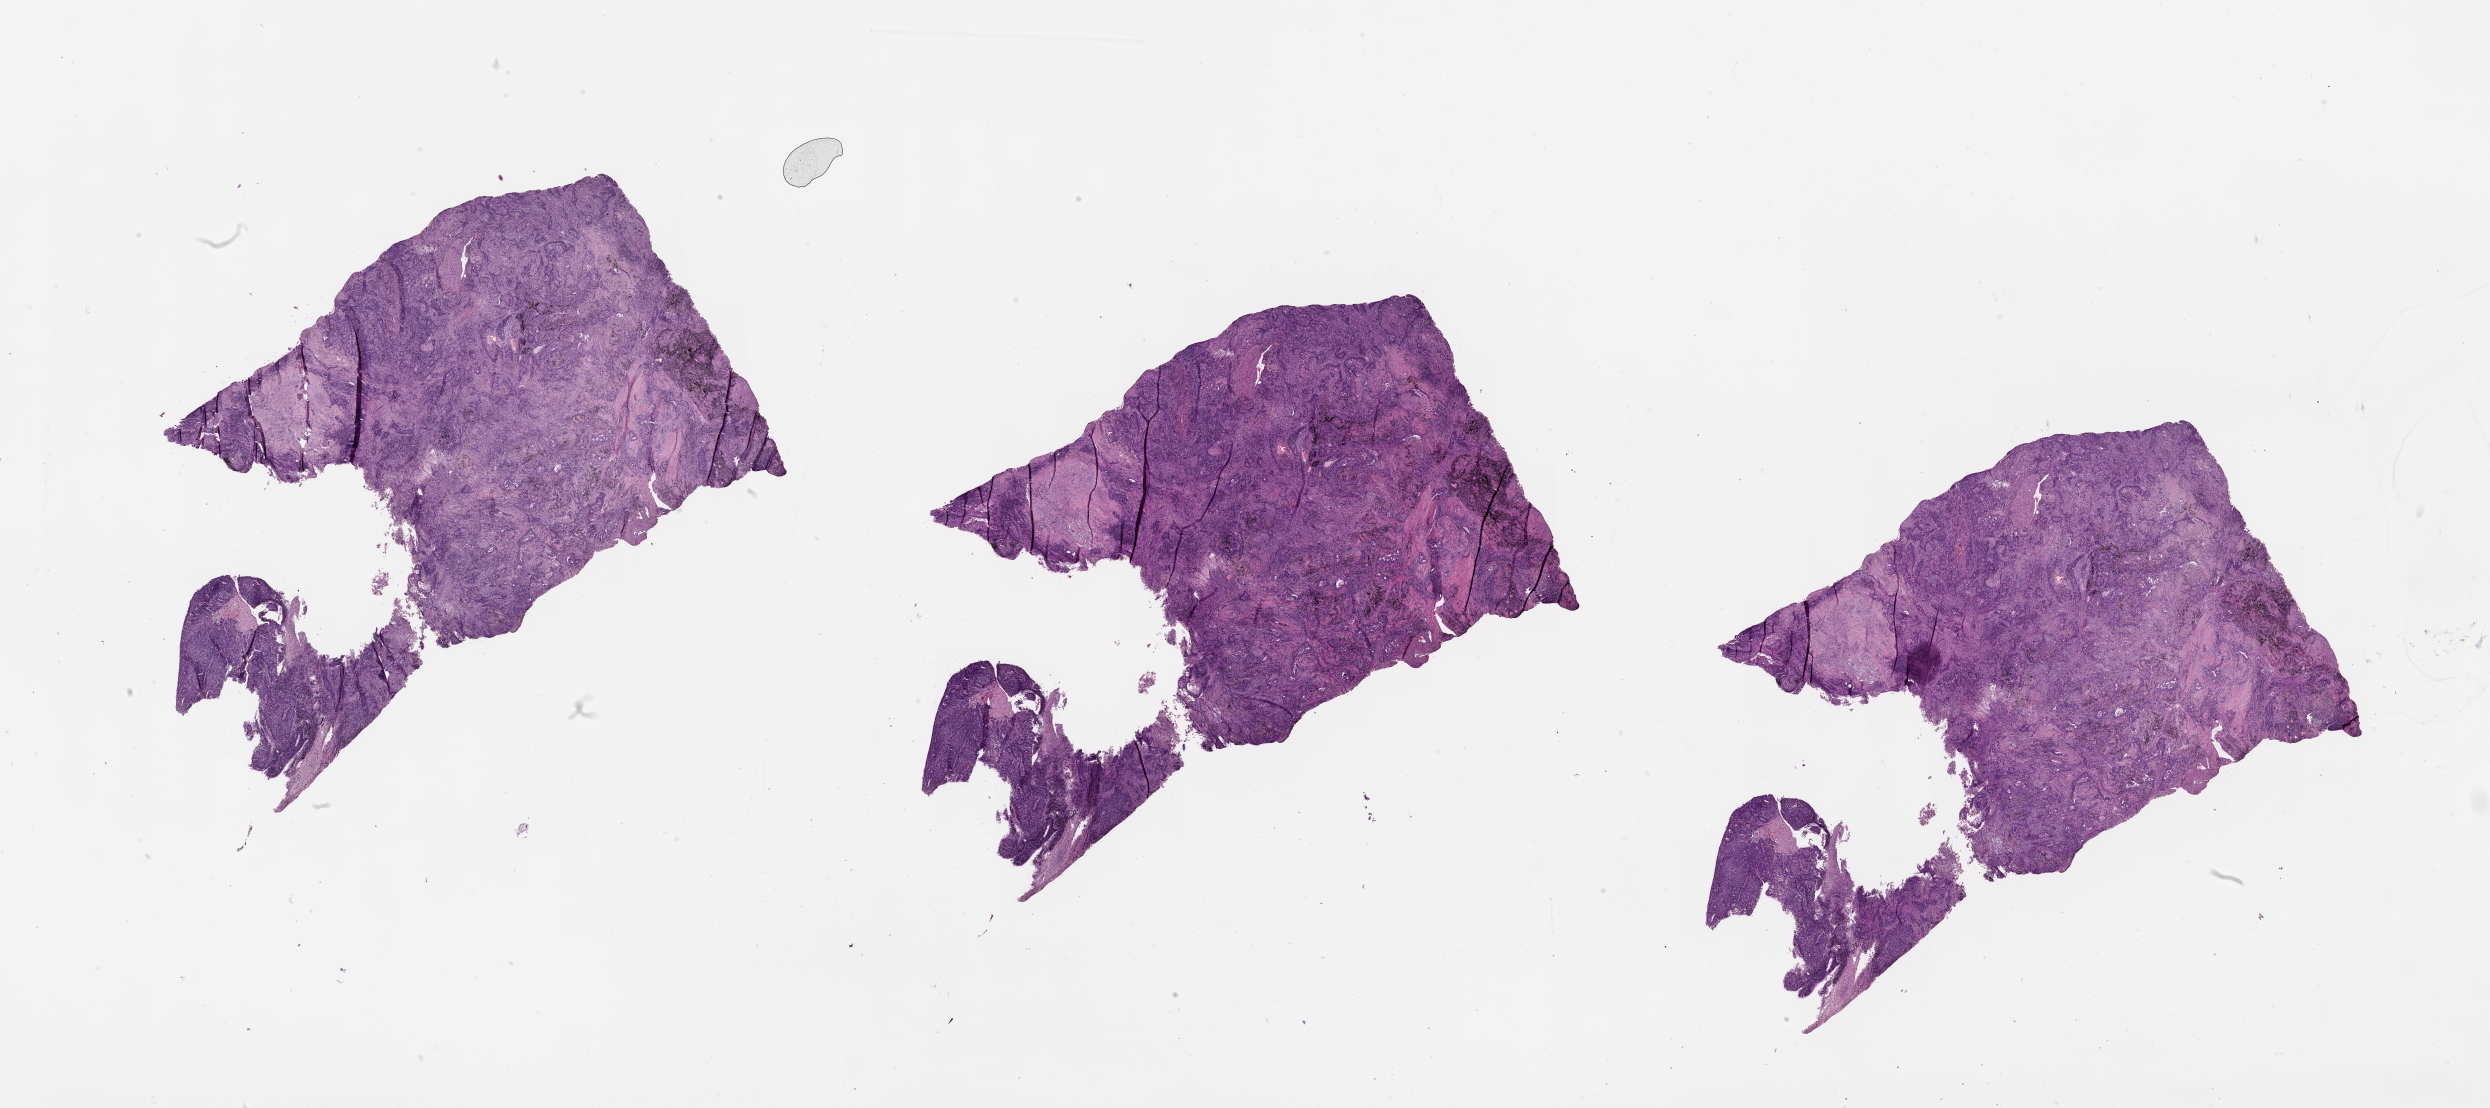
Digitized H&E-stained tissue section (whole slide) — a low-resolution overview of the entire scanned area, about 40.1 x 17.8 mm, tumour tissue sample, lung. Male, 66 y/o.
Patient diagnosis (cohort enrolment): squamous cell carcinoma (lung).